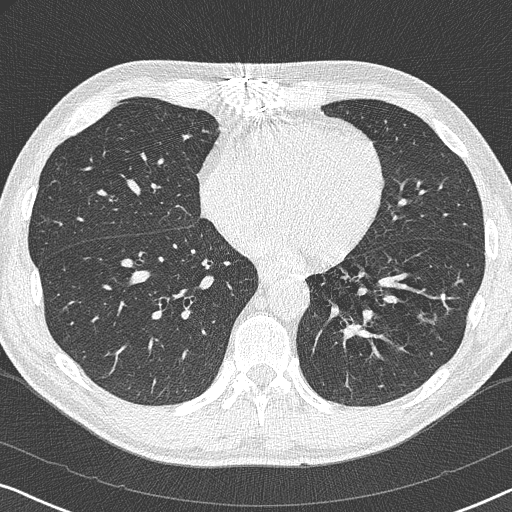
Low-dose screening chest CT, axial slice. Baseline screening round. Lung window (W 1500 / L -600 HU). 1 mm slice thickness. Lung (sharp) reconstruction kernel (B50f). 512 × 512 image matrix, field of view 330 × 330 mm. Male participant, aged 59 years at enrolment. Current smoker at enrolment.
Lesion marked by an expert reader, bounding box (x1, y1, x2, y2) in pixels: (407, 304, 449, 335). The screening reader recorded 2 non-calcified nodules or masses ≥4 mm on this exam; which of them this box marks is not recorded.